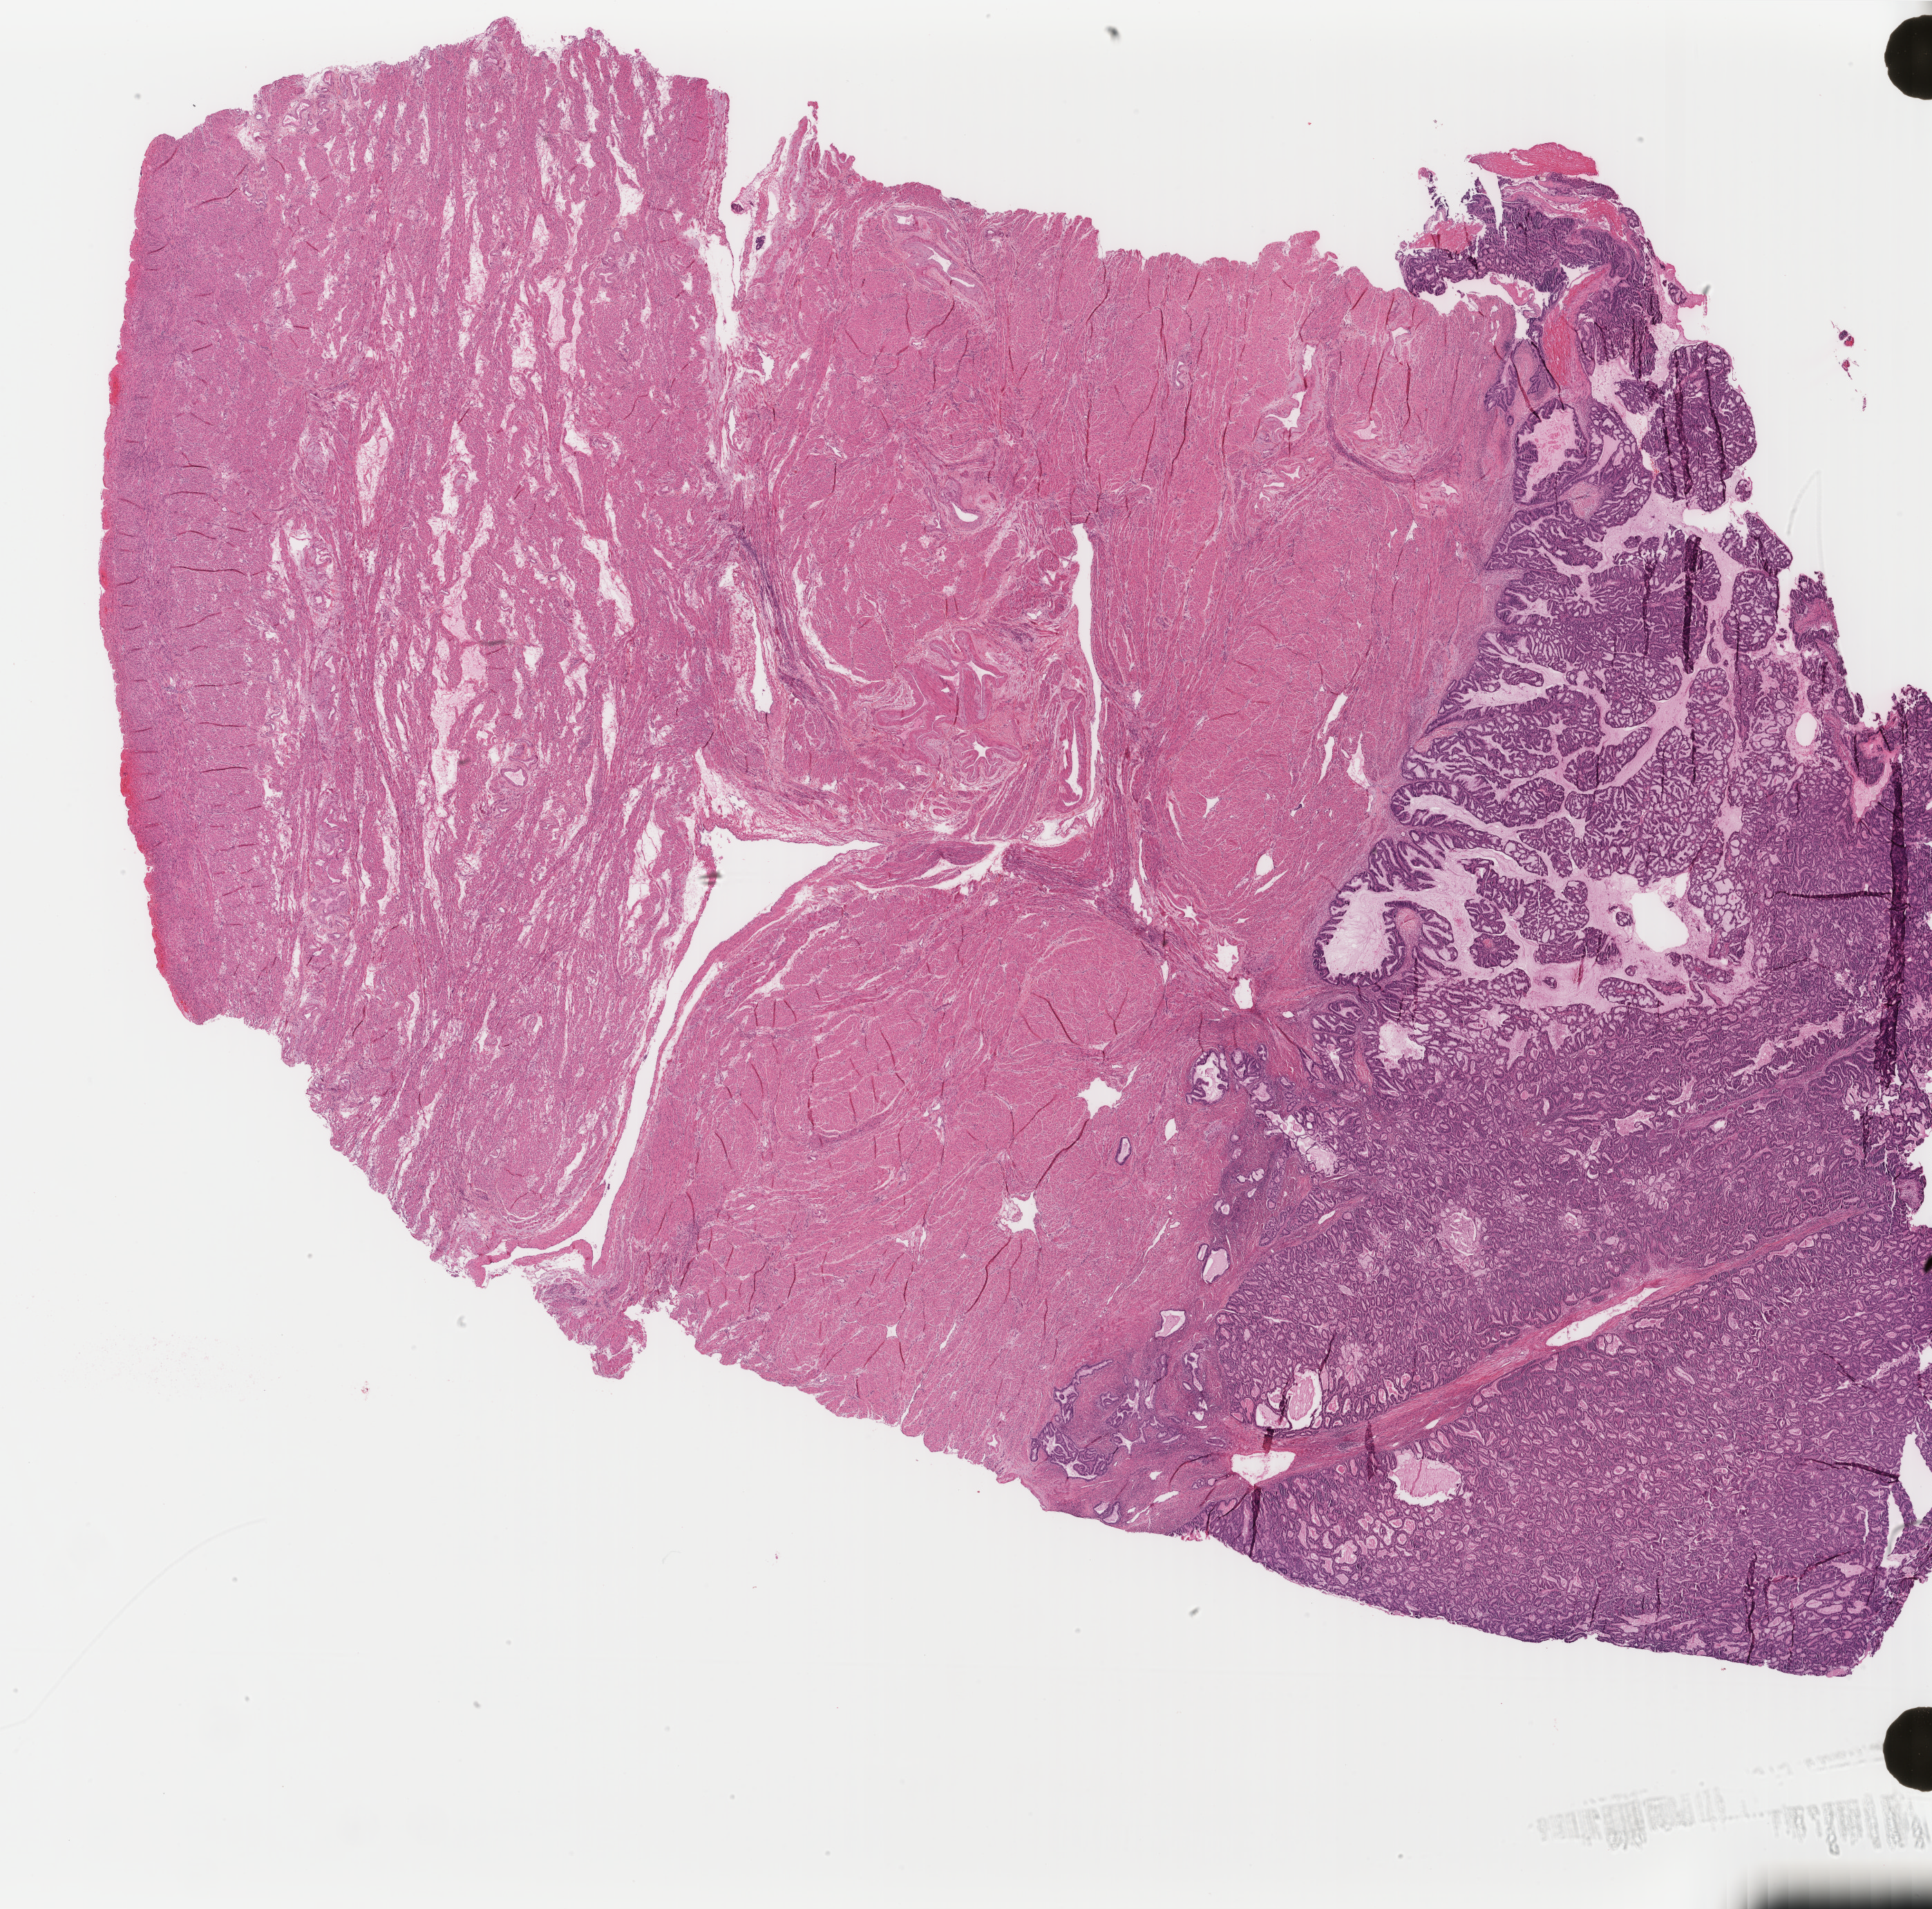
Whole-slide histology image, H&E, whole scanned area (about 22.2 x 21.9 mm, slide scanned at 40x) shown as a low-resolution overview. FFPE section. Sample: primary tumour, uterus. Patient: female, age at initial diagnosis 61 years. Histologic grade: G1 (well differentiated).
Pathologic diagnosis: Endometrioid adenocarcinoma, NOS (endometrium). FIGO stage: IB. Lymph nodes positive (case pathology): 0 of 3 examined.